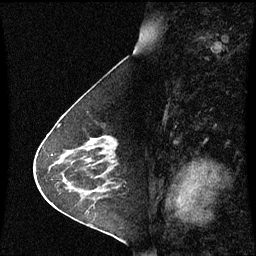
Breast MRI (dynamic contrast-enhanced), one sagittal slice. Position 28 of 60 along the scan axis. Dynamic contrast-enhanced series, image 2 of 3 at this slice position (ordered by acquisition). 1.5 T. TE 4.2 ms, TR 8.9 ms. 2 mm slice thickness. 256 × 256 image matrix, field of view 210 × 210 mm. Female patient, age 63 years. From the clinical record (not read from this slice): setting: breast cancer imaged before/during neoadjuvant chemotherapy; receptor status: HR-positive, HER2-negative.
Annotated regions visible in this slice (semi-automatically segmented with operator editing):
- analysis volume of interest (the breast-tissue region the enhancement analysis was run in; not a lesion): box from (x=76, y=137) to (x=119, y=178) px
- tumour enhancement mask (voxels above the 70 % enhancement threshold inside the analysis volume of interest): (x=109, y=139)–(x=114, y=163)